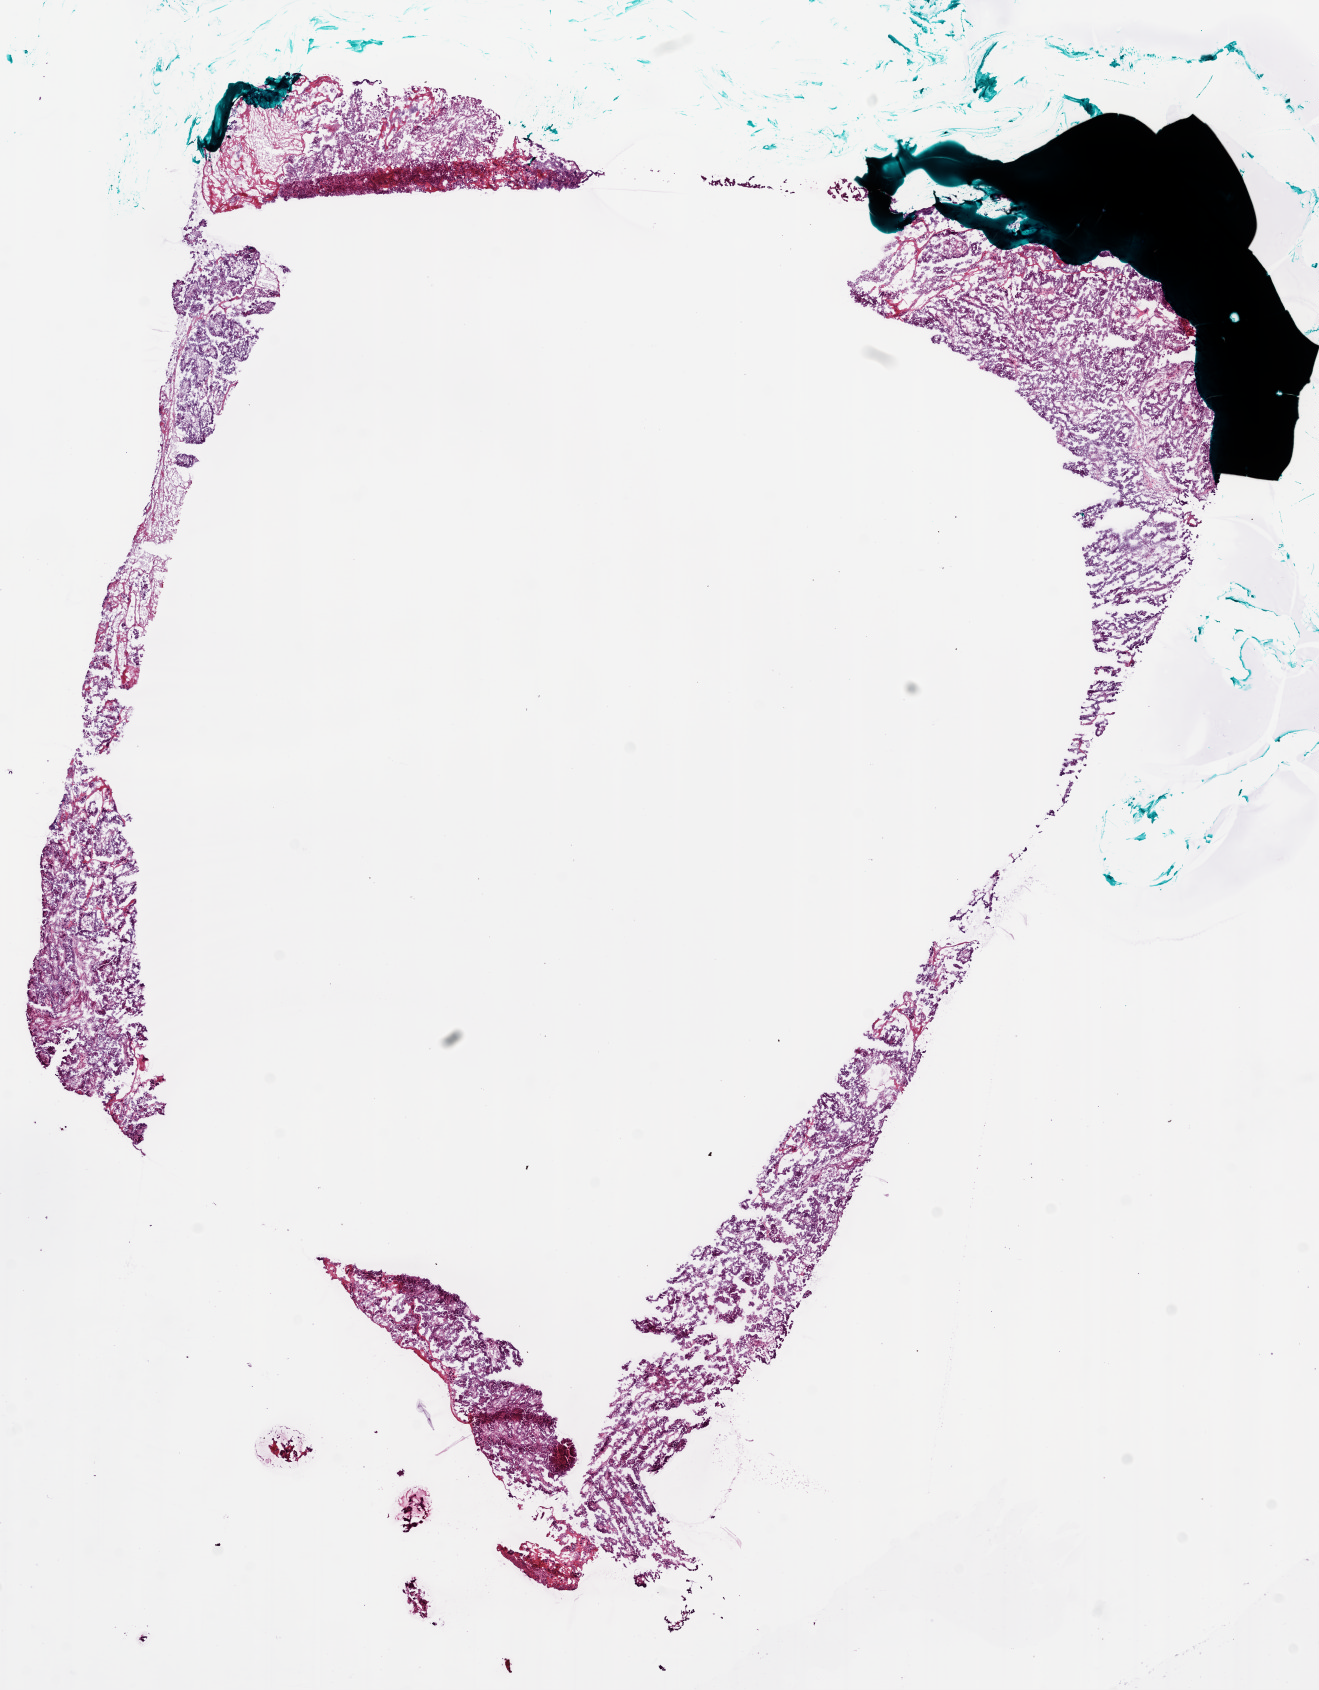
H&E-stained whole-slide image, whole scanned area (about 10.6 x 13.6 mm, acquisition: 20x scan) shown as a low-resolution overview. Frozen section from the bottom of the tissue portion. Ovary, primary tumour sample. Female patient; age at initial diagnosis 51 years. Histologic grade: G3 (poorly differentiated). Slide review estimates, as recorded: tumour cells 94%, tumour nuclei 95%, normal cells 5%, necrosis 1%.
• laterality: bilateral
• FIGO stage: IV
• histologic diagnosis: Serous cystadenocarcinoma, NOS